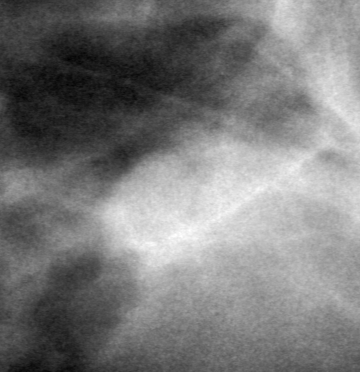
Cropped region of a digitized screen-film mammogram centred on a radiologist-marked abnormality; left breast; MLO view; BI-RADS breast density category 3 (scale 1–4).
- Mass, shape lobulated, margins circumscribed; BI-RADS assessment category 0 (incomplete: needs additional imaging); pathology result (as recorded, not read from the image): benign.